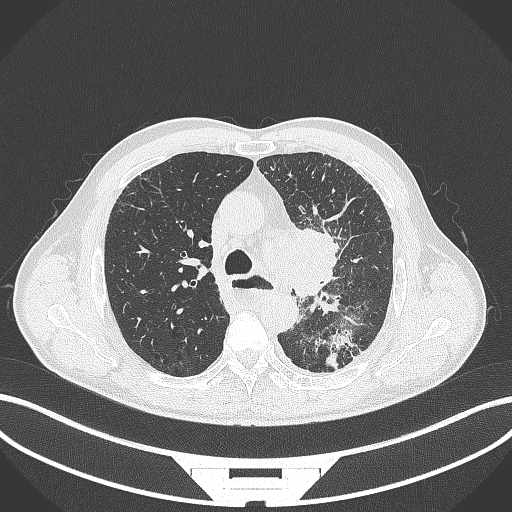
Chest CT, one axial slice; slice 263 of 411 in the series (ordered by position); lung window (W 1500 / L -600 HU); 1 mm slice thickness; 512 × 512 image matrix, field of view 400 × 400 mm. Patient: male, 57 years. Case-level facts recorded for this patient, not image findings: clinical TNM (as recorded): T2a N1 M0.
Outlined on this slice (bounding box drawn by a radiologist):
- lung tumour (recorded histology: squamous cell carcinoma): box from (x=289, y=223) to (x=342, y=304) px